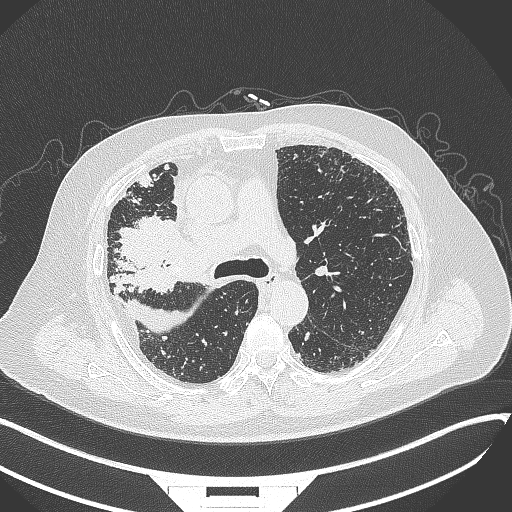
Chest CT, one axial slice; slice 223 of 384 in the series (ordered by position); 120 kVp; lung window (W 1500 / L -600 HU); 1 mm slice thickness; 512 × 512 image matrix, field of view 400 × 400 mm. Patient: male, 69 years. From the clinical record (not read from this slice): clinical TNM (as recorded): T4 N3 M1.
Structures marked on this image (bounding box drawn by a radiologist):
- lung tumour (recorded histology: adenocarcinoma): bounding box <119,213,186,274> (left, top, right, bottom; pixels)